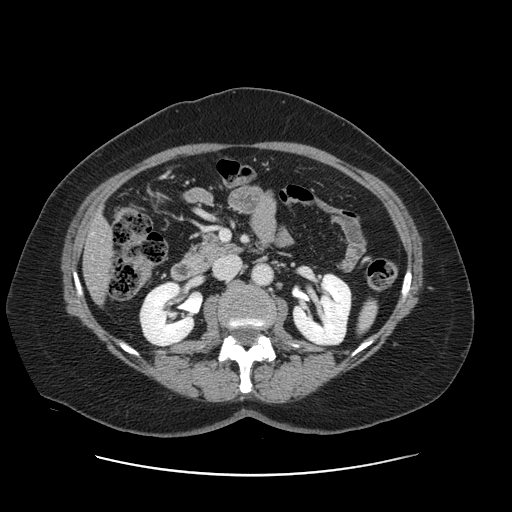
Contrast-enhanced abdominal CT, one axial slice. Slice 52 of 161 in the series (ordered by position). 120 kVp. Intravenous contrast given. Soft-tissue window (W 400 / L 40 HU). 2.5 mm slice thickness. 512 × 512 image matrix, field of view 398 × 398 mm. Female patient, age 62 years. Case-level facts recorded for this patient, not image findings: diagnosis: colorectal cancer liver metastases, imaged before liver resection; multiple liver metastases: no.
Annotated regions visible in this slice (manually delineated by an expert):
- liver: bounding box (x1, y1, x2, y2) in pixels: (84, 217, 111, 300)